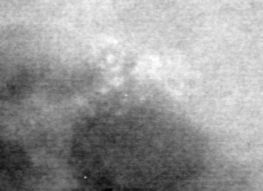
Cropped region of a digitized screen-film mammogram centred on a radiologist-marked abnormality, right breast, MLO view.
Marked abnormality: calcifications, morphology pleomorphic, distribution clustered; BI-RADS assessment category 4; subtlety rating 3 on a 1 (subtle) to 5 (obvious) scale; pathology result (as recorded, not read from the image): malignant.